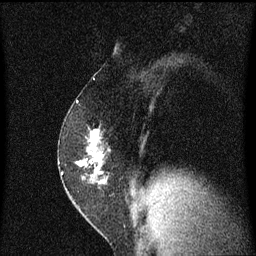
Breast MRI (dynamic contrast-enhanced), one sagittal slice. Position 37 of 60 along the scan axis. Dynamic contrast-enhanced series, image 2 of 3 at this slice position (ordered by acquisition). 1.5 T. TE 4.2 ms, TR 8.4 ms. 2 mm slice thickness. 256 × 256 image matrix, field of view 200 × 200 mm. Patient: female, 52 years. From the clinical record (not read from this slice): setting: breast cancer imaged before/during neoadjuvant chemotherapy; receptor status: HER2-positive.
Annotated regions visible in this slice (semi-automatic segmentation, software-assisted and operator-edited):
- analysis volume of interest (the breast-tissue region the enhancement analysis was run in; not a lesion): bounding box (x1, y1, x2, y2) in pixels: (59, 124, 113, 191)
- tumour enhancement mask (voxels above the 70 % enhancement threshold inside the analysis volume of interest): (80, 130, 101, 183)